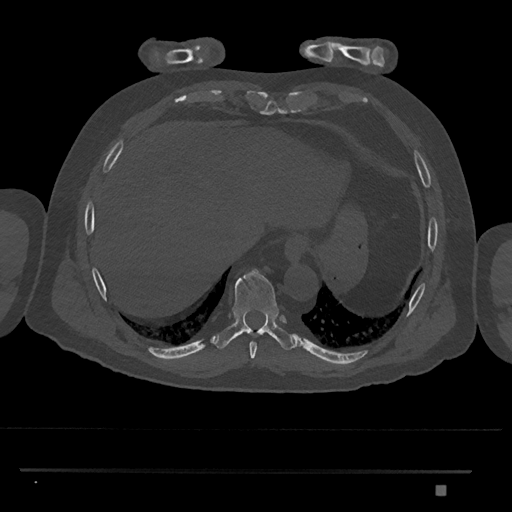
CT including the spine, one axial slice; position 1069 of 1134 along the scan axis; reconstruction kernel Br40s/3; bone window (W 1800 / L 400 HU); 0.5 mm slice thickness; 512 × 512 image matrix. Male patient, age 65 years. Case-level facts recorded for this patient, not image findings: primary cancer: prostate.
Annotated regions visible in this slice (semi-automatic segmentation, software-assisted and operator-edited):
- T8 vertebra: bounding box <250,342,257,360> (left, top, right, bottom; pixels)
- T9 vertebra: <215,269,295,350>